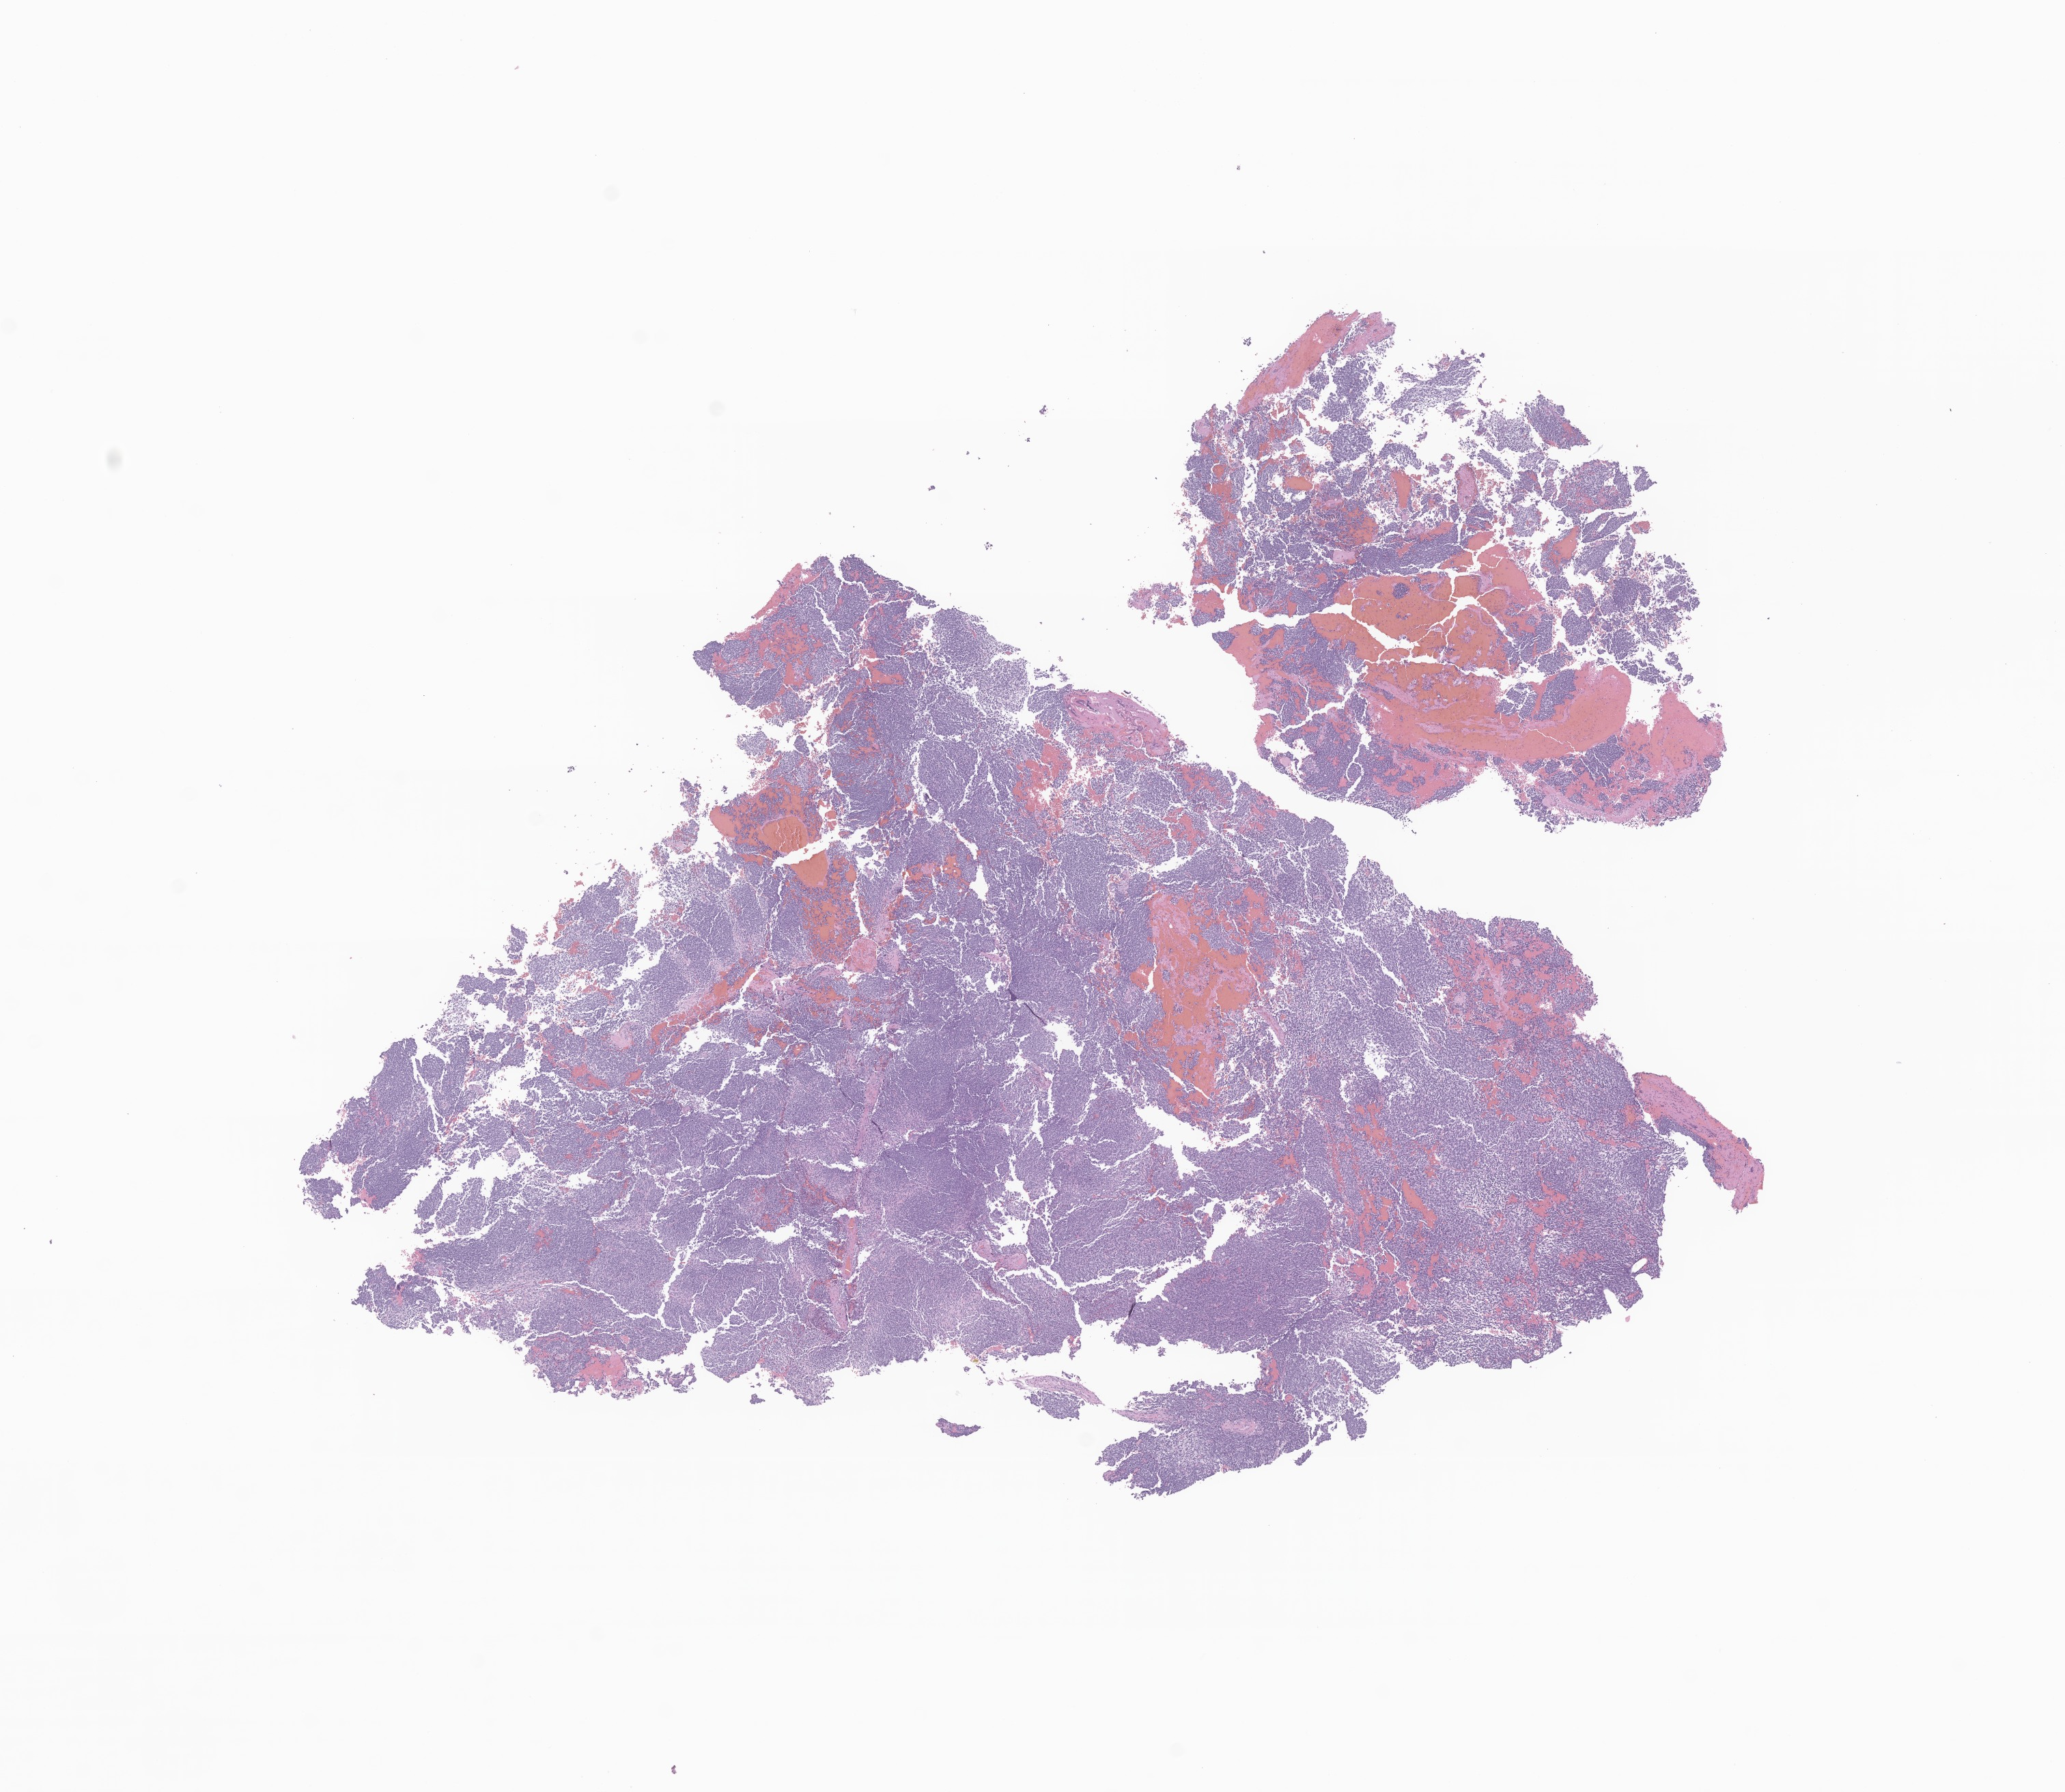
Whole-slide image, H&E stain of tumor tissue from the brain, a low-resolution overview of the entire scanned area, about 12.7 x 11.1 mm; FFPE section. Patient: male, age 195 months (16 years 3 months).
- recorded diagnosis: Medulloblastoma, NOS